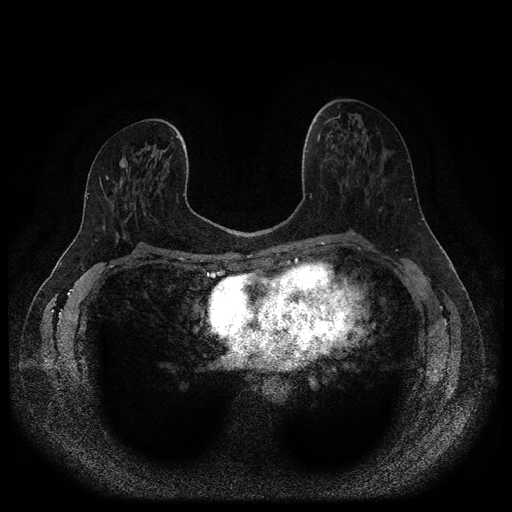
Breast MRI (dynamic contrast-enhanced, multi-phase), one axial slice; slice 51 of 116 in the series (ordered by position); dynamic contrast-enhanced series, time point 2 of 5 at this slice position (early post-contrast); 1.5 T; TE 2.7 ms, TR 5.4 ms; 2 mm slice thickness; 512 × 512 image matrix. Female patient, age 46 years.
Structures marked on this image (semi-automatically segmented with operator editing):
- breast lesion (labelled benign in the annotation): bounding box (x1, y1, x2, y2) in pixels: (119, 158, 127, 168)